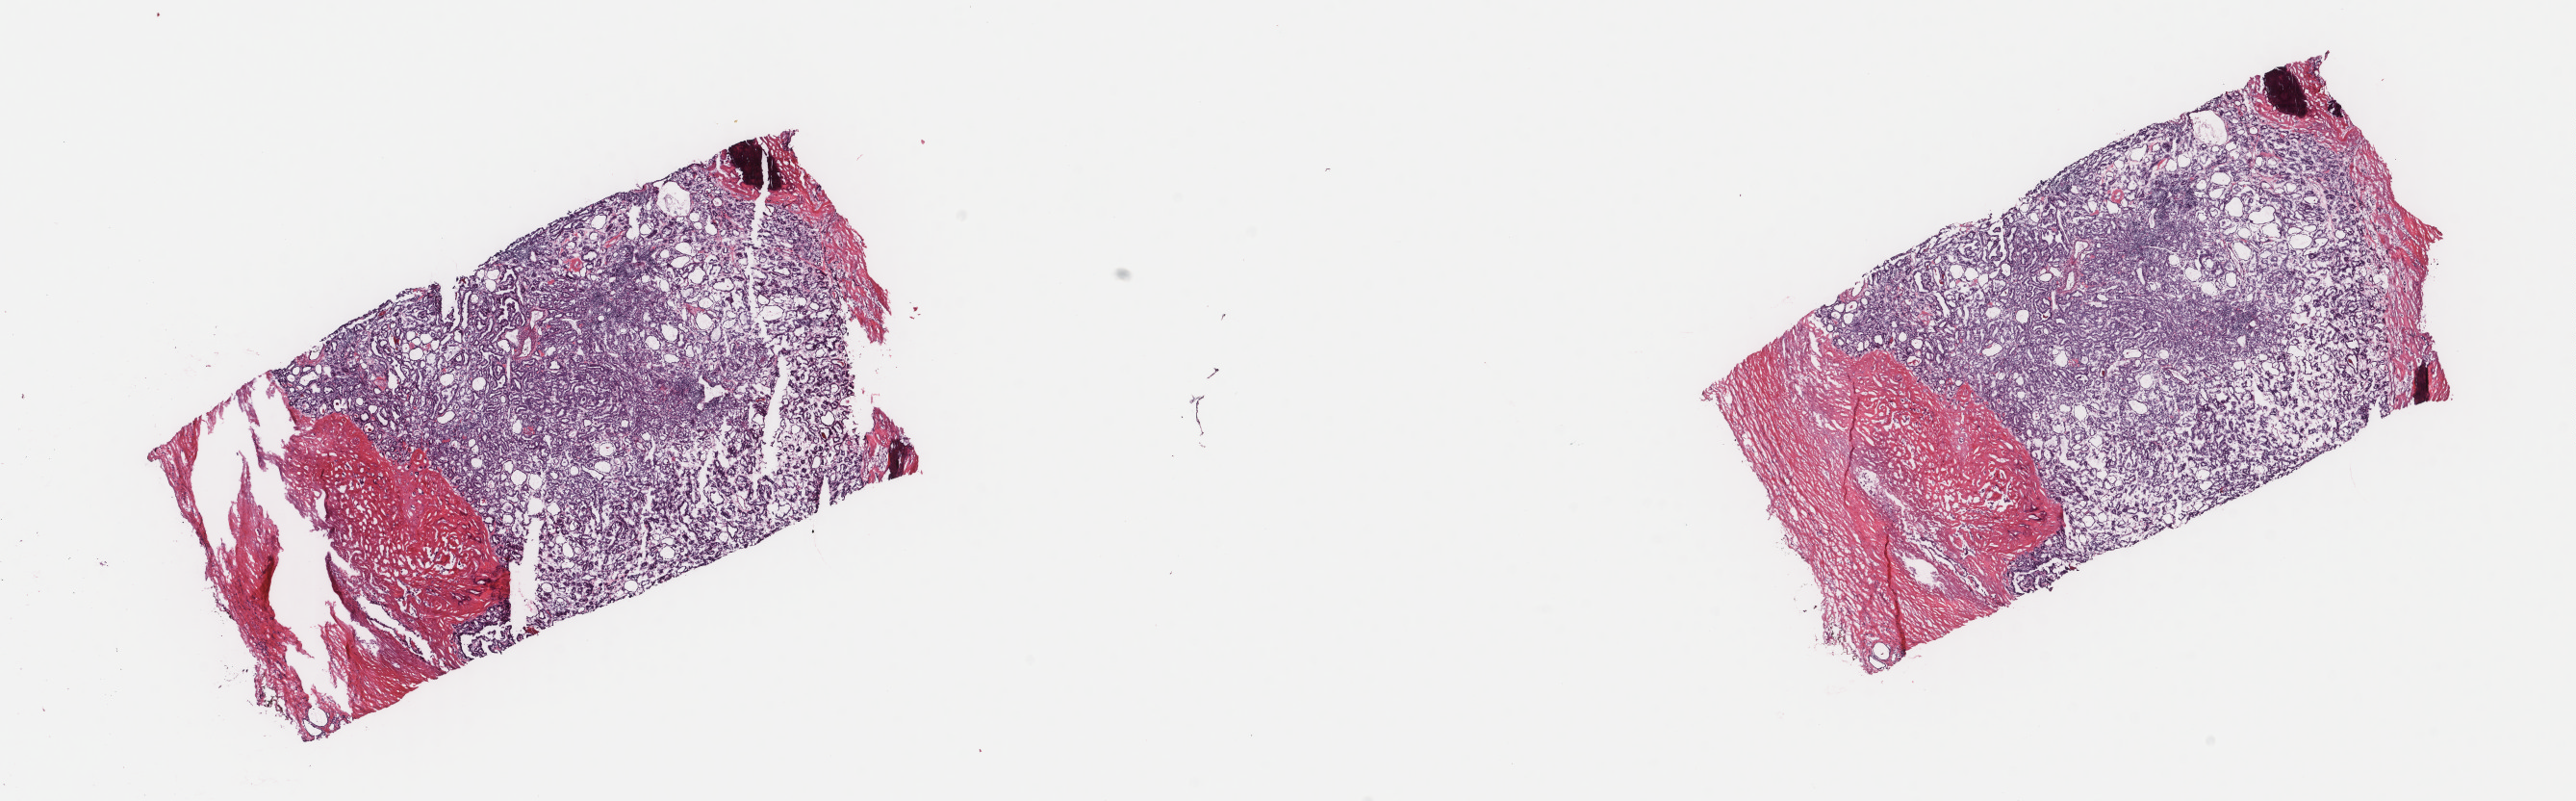
H&E whole-slide image, a low-resolution overview of the entire scanned area, about 21.2 x 6.6 mm (from a 40x scan); frozen section from the top of the tissue portion; thyroid, primary tumour sample. Patient: male, age at initial diagnosis 54 years. Composition of this section per pathologist review: tumour cells 75%, tumour nuclei 90%, normal cells 0%, stromal cells 25%, necrosis 0%. Infiltration values recorded for this section: lymphocyte infiltration 0%, monocyte infiltration 0%, neutrophil infiltration 0%.
Histologic diagnosis: Papillary adenocarcinoma, NOS (thyroid gland). Laterality: bilateral. AJCC pathologic stage: I (7th edition).